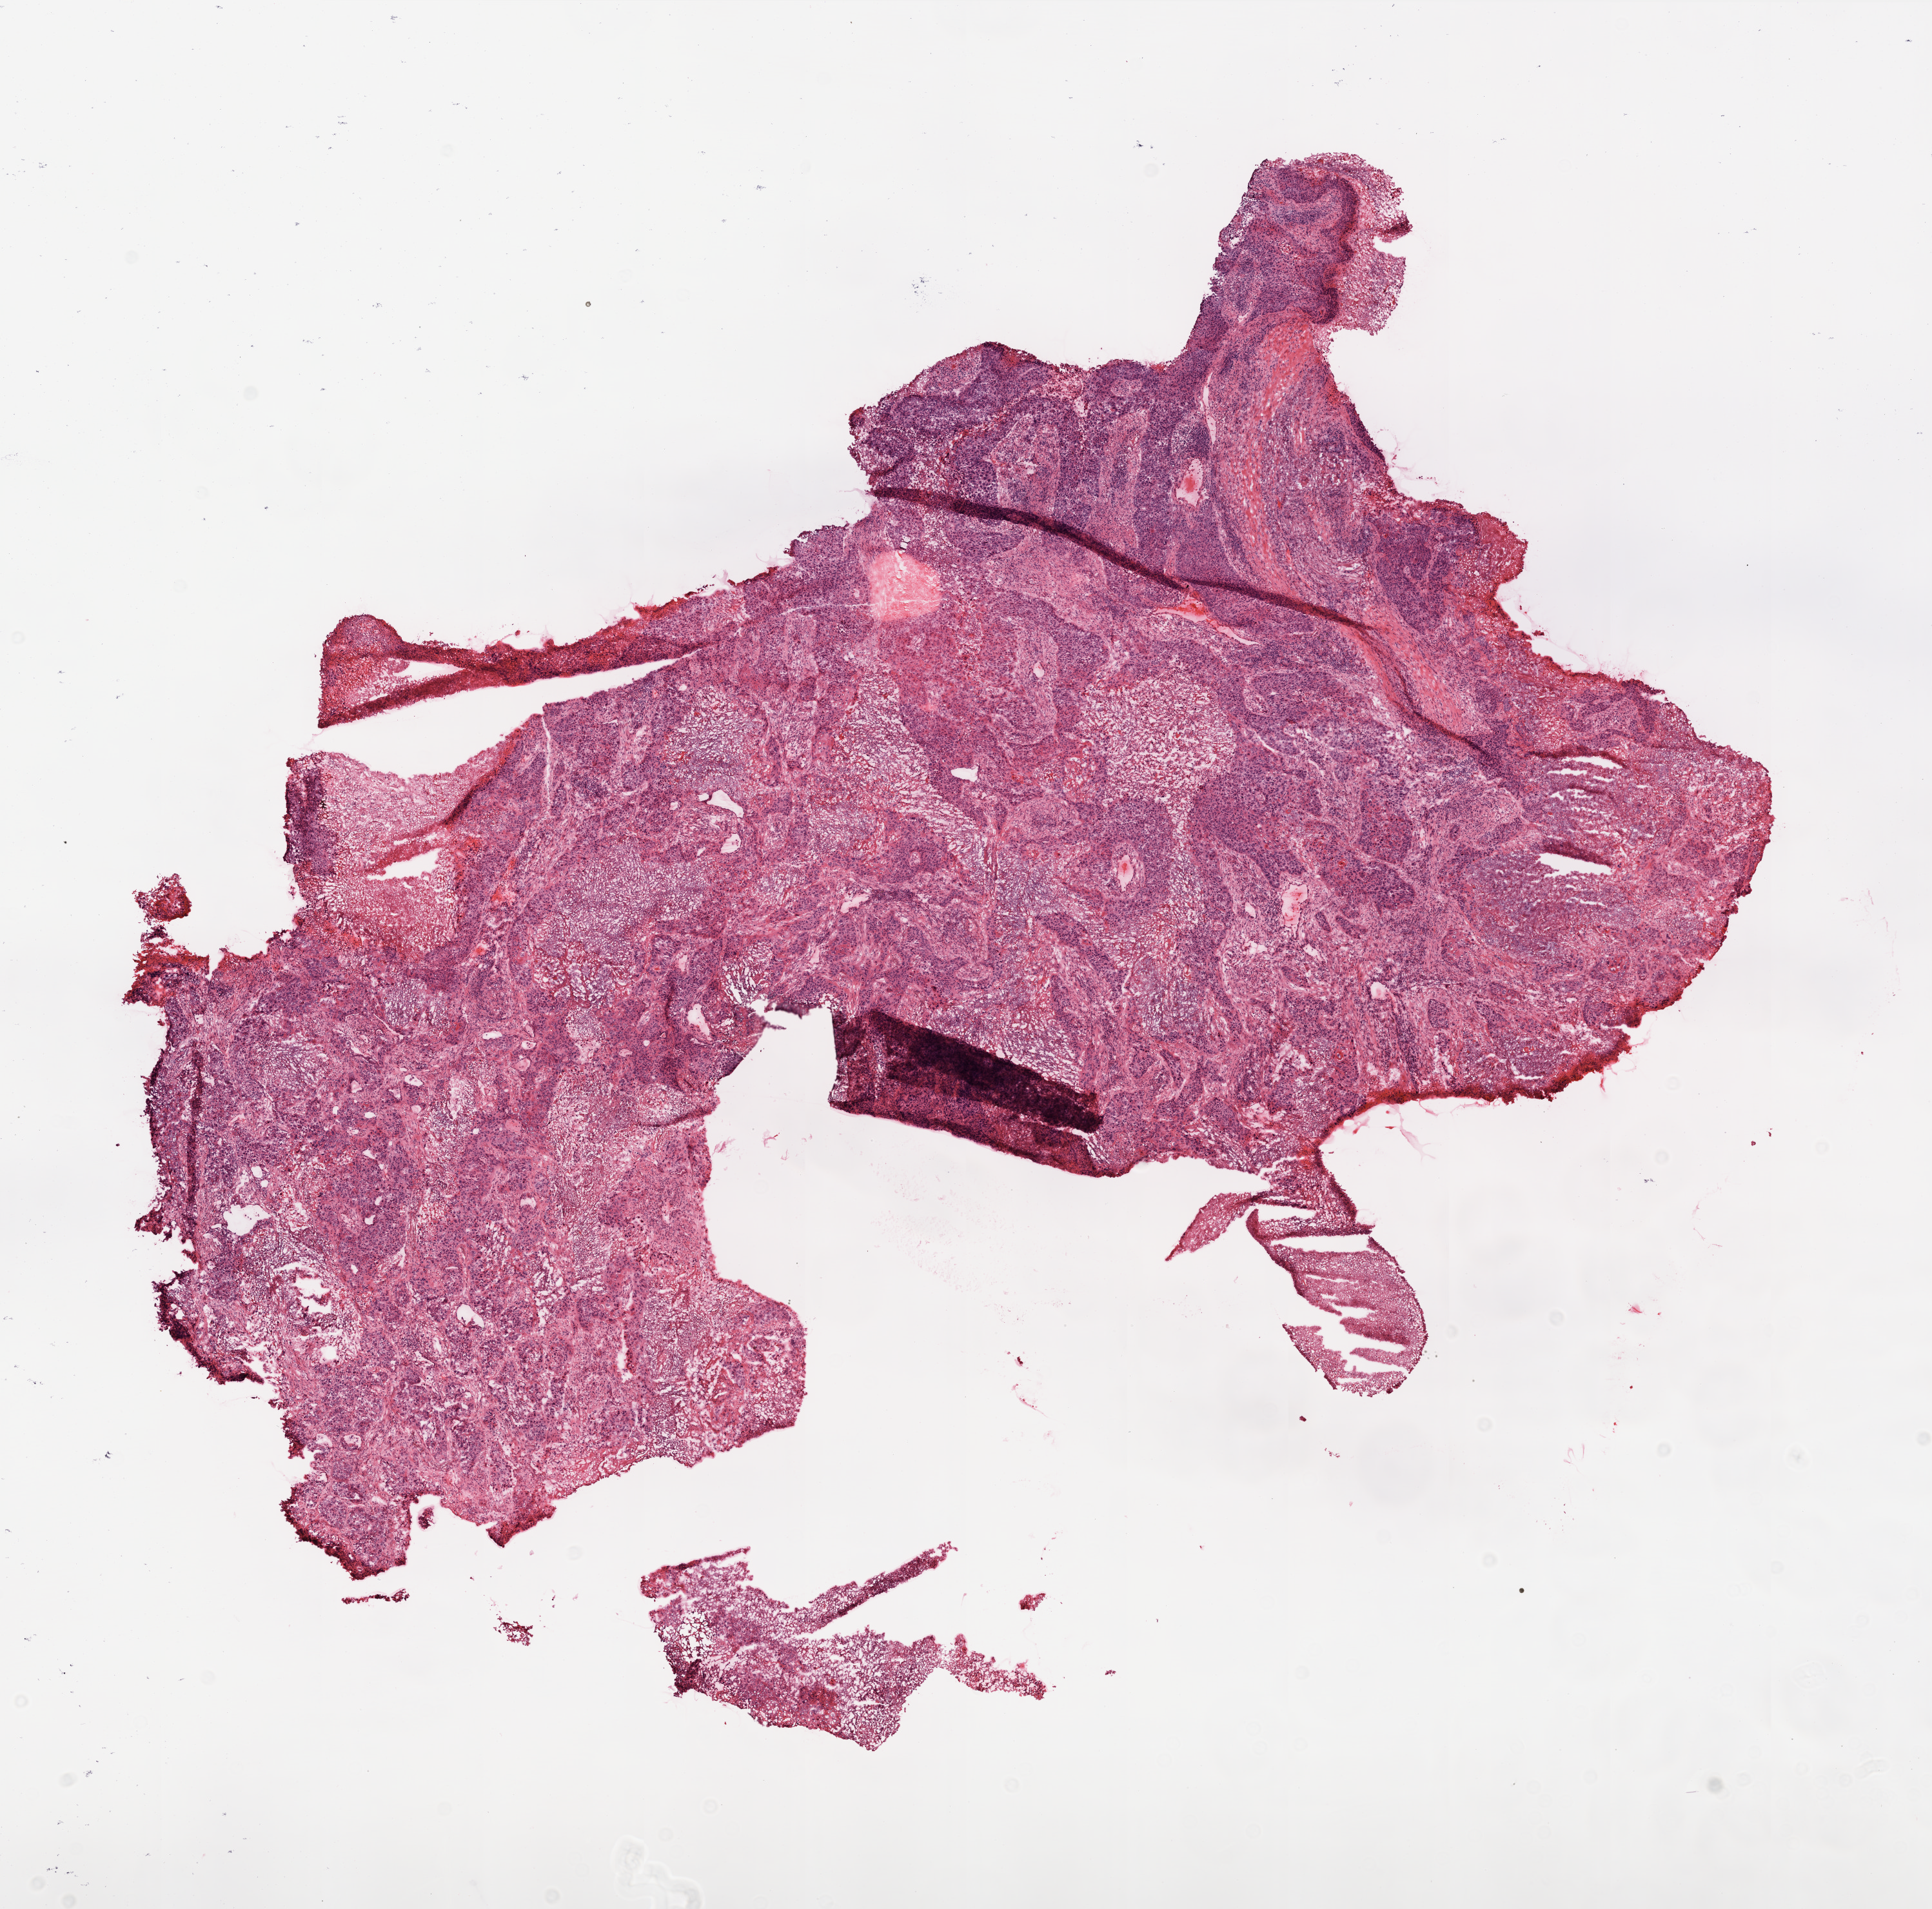
Hematoxylin and eosin (H&E) stained whole-slide image — shown as a low-resolution overview of the whole scanned area (about 12.0 x 11.8 mm, slide scanned at 20x), frozen section, sample: primary tumour, lung. Male, age 67 years at initial diagnosis. Composition of this section per pathologist review: tumour nuclei 85%, necrosis 10%.
Diagnosis: Squamous cell carcinoma, NOS (upper lobe, lung).